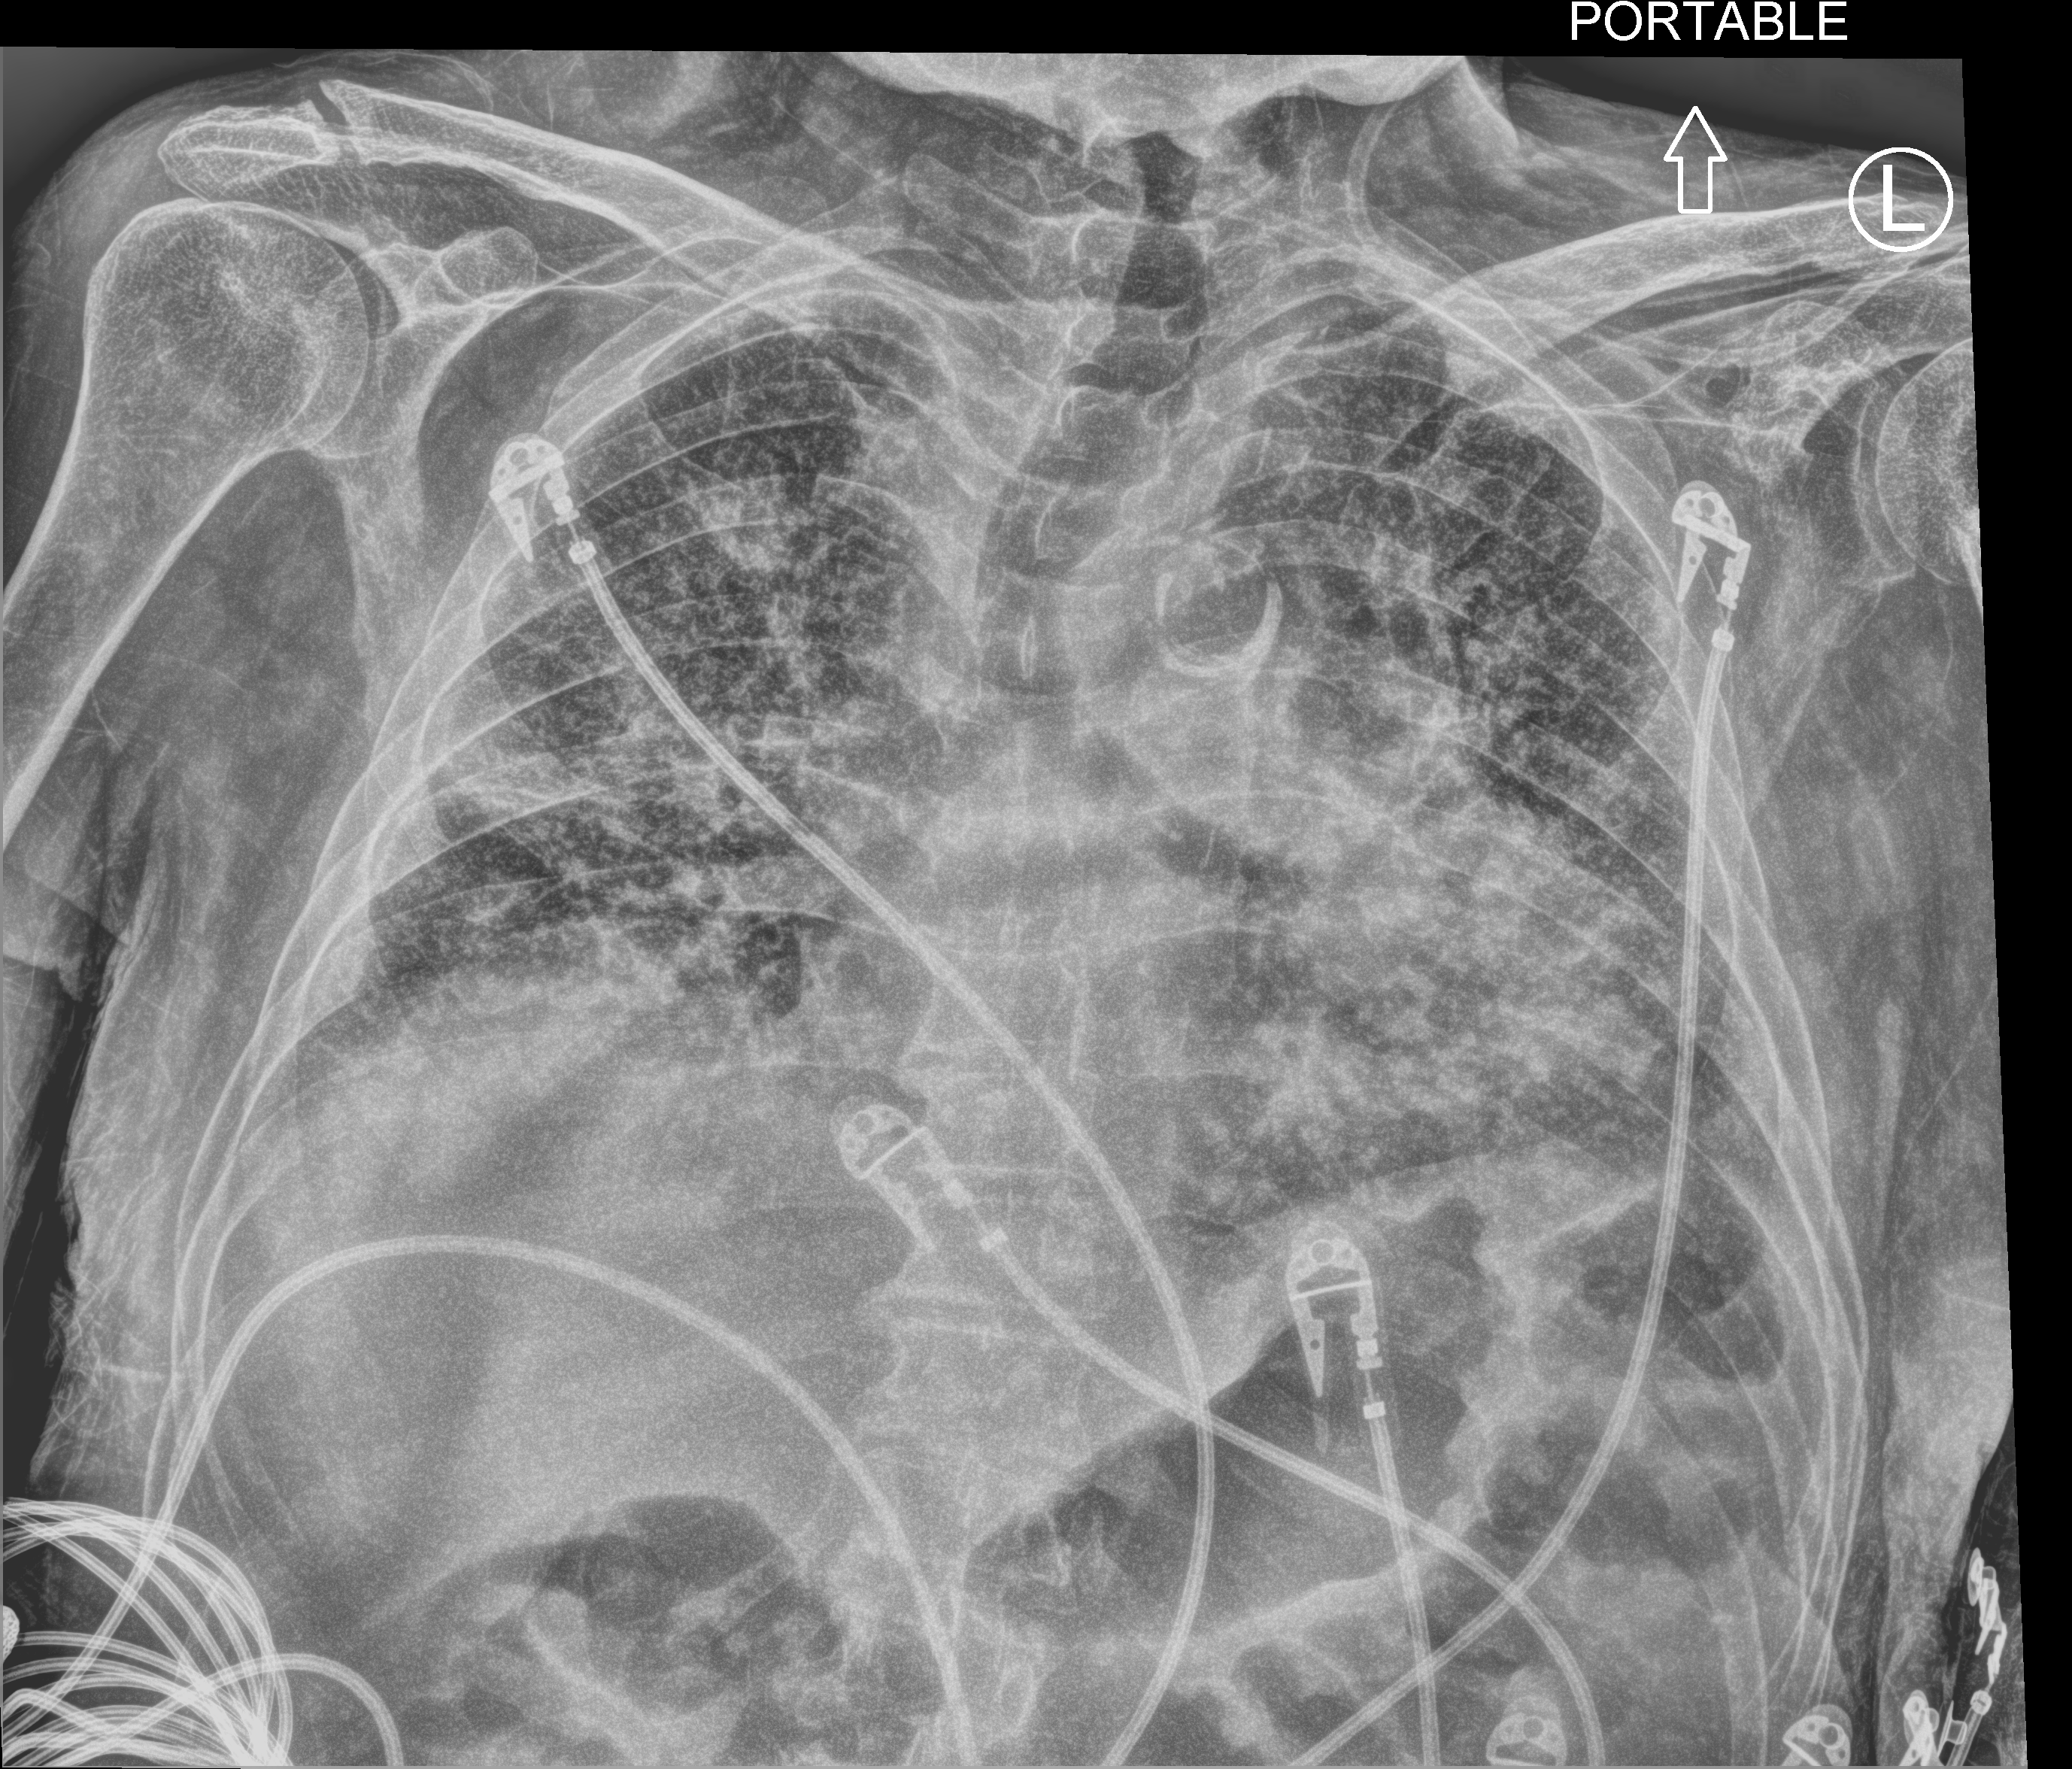
Chest X-ray (portable), anteroposterior (AP) projection. Patient hospitalised with COVID-19; male, aged 60–74 years.
From the hospital-stay record, not from the radiograph (when in the stay this image was taken is not recorded):
- mechanically ventilated during this hospital stay: no
- chronic kidney disease (admission record): no
- other chronic lung disease (admission record): no